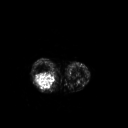
FDG PET of an extremity soft-tissue mass (from a PET/CT study), one axial slice. Slice 176 of 267 in the series (ordered by position). 3.27 mm slice thickness. 128 × 128 image matrix, field of view 500 × 500 mm. Female patient, age 62 years. Case-level facts recorded for this patient, not image findings: histological type: liposarcoma; site of the primary tumour: right thigh.
Annotated regions visible in this slice (expert contour drawn on MRI and transferred to this co-registered scan by the dataset authors):
- gross tumour volume (mass): box from (x=35, y=73) to (x=56, y=90) px